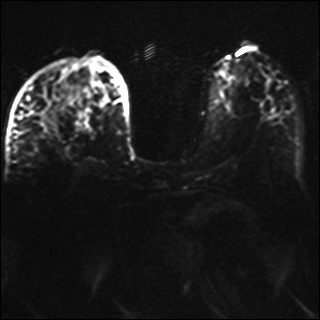
Breast MRI, one axial slice. Position 17 of 42 along the scan axis. Diffusion-weighted series; image 2 of 4 stored at this slice position (different b-values; order by instance number). 1.5 T. 4 mm slice thickness. 320 × 320 image matrix, field of view 330 × 330 mm. Female patient.
Annotated regions visible in this slice (outlined manually by an expert reader):
- tumour on diffusion-weighted imaging: box from (x=40, y=116) to (x=54, y=131) px